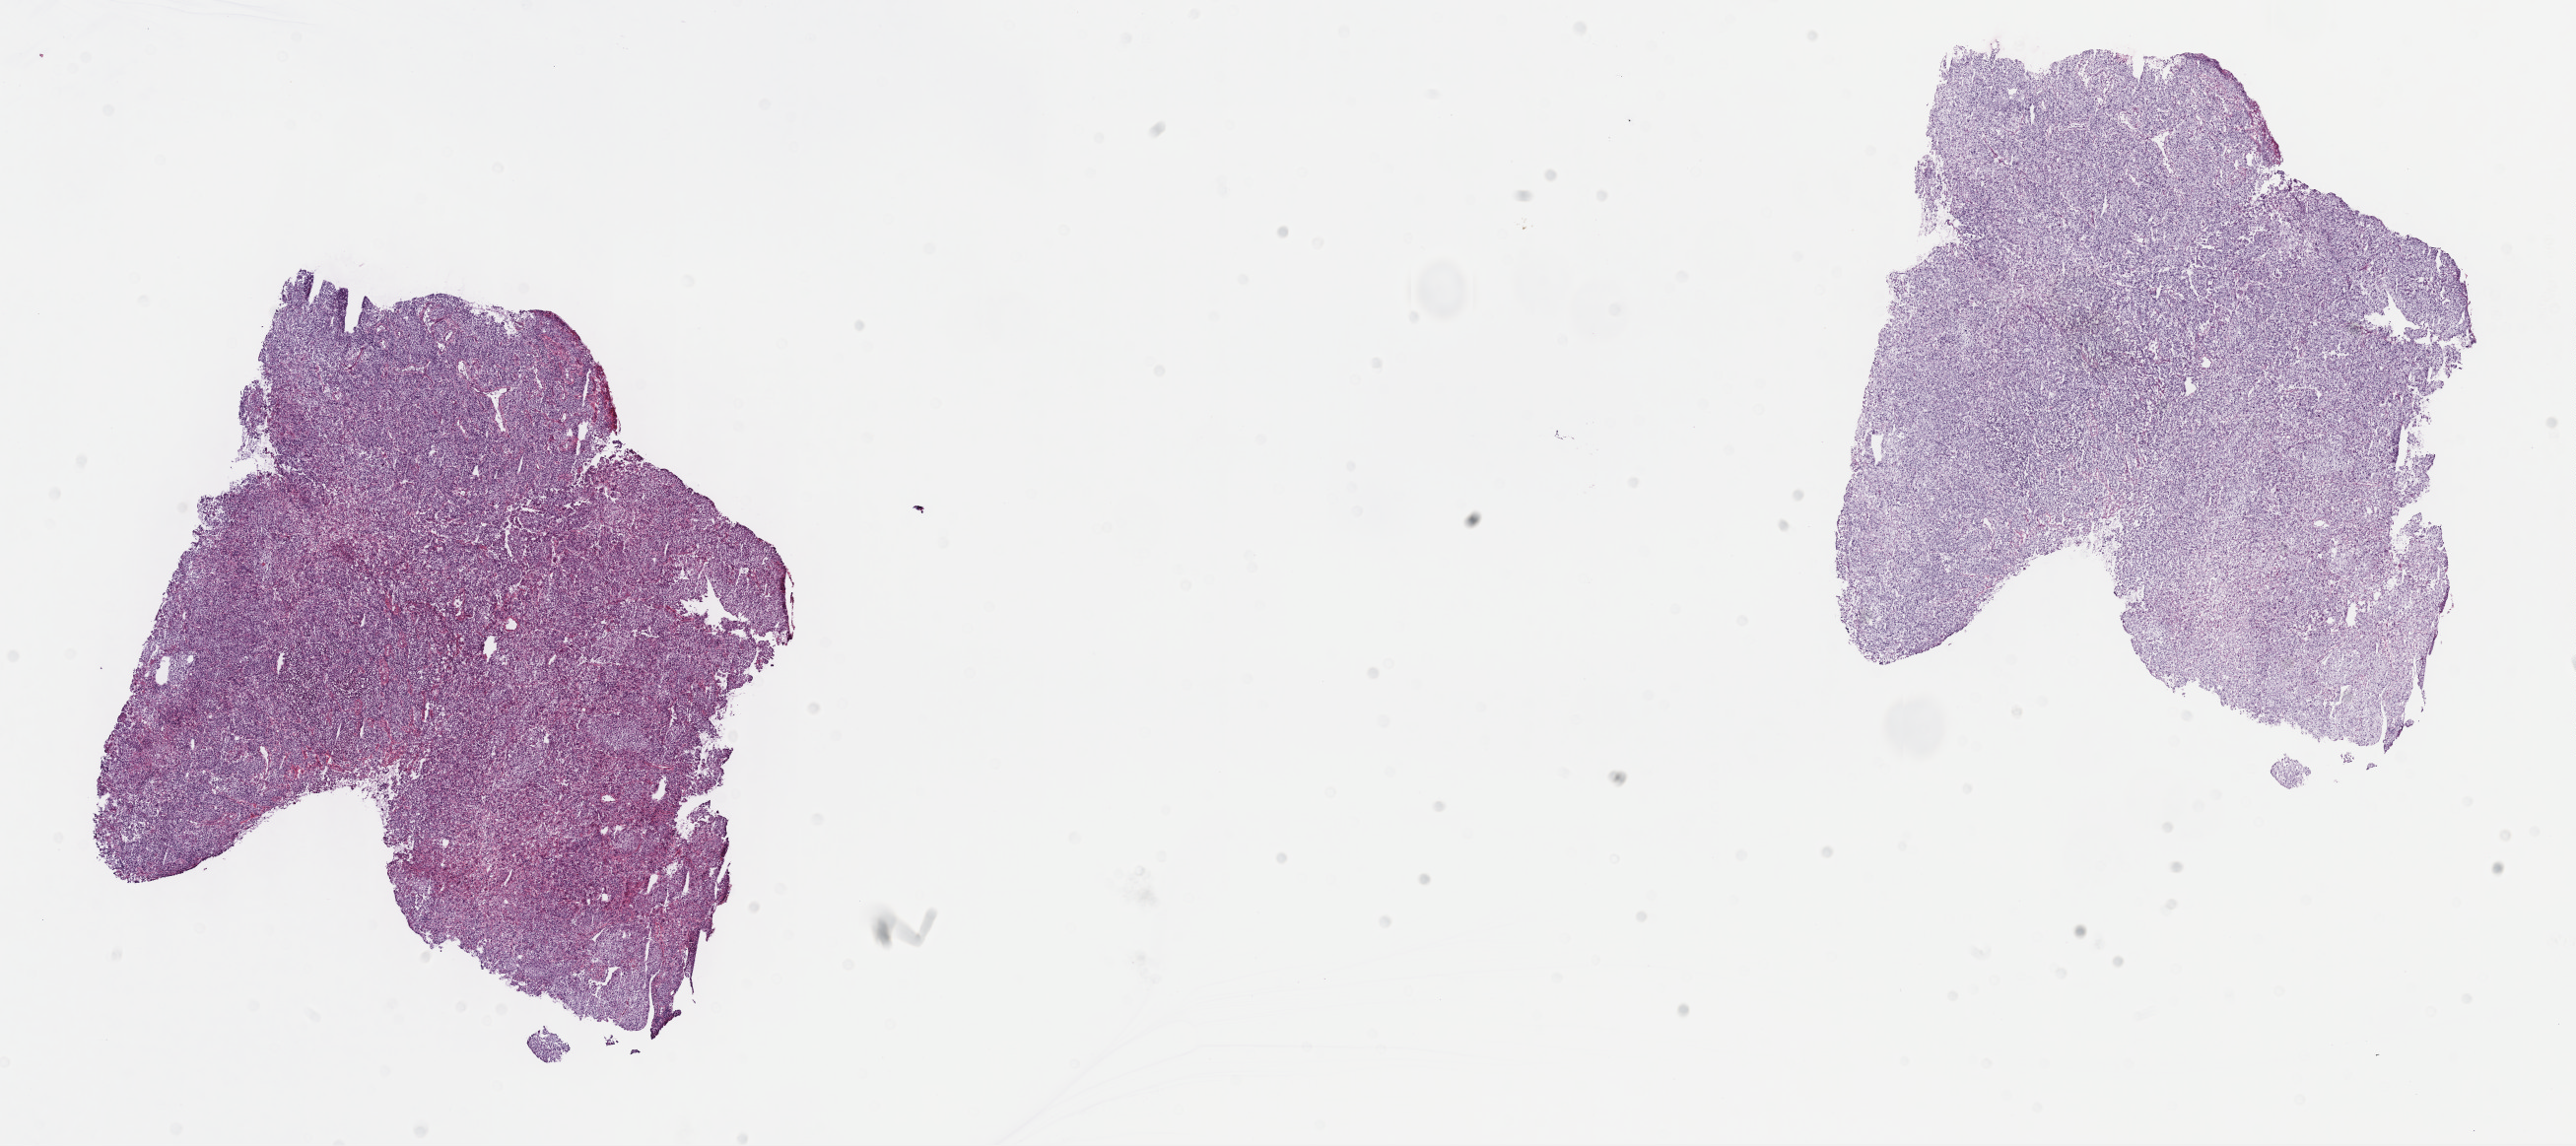
Digitized H&E-stained tissue section (whole slide), low-resolution overview of the scanned area, about 21.1 x 9.4 mm (acquisition: 40x scan); frozen section from the top of the tissue portion; sample: primary tumour, cervix. Female, age 32 years at initial diagnosis. Histologic grade: G2 (moderately differentiated). Composition of this section per pathologist review: tumour cells 90%, tumour nuclei 90%, normal cells 0%, stromal cells 10%, necrosis 0%. Infiltration values recorded for this section: lymphocyte infiltration 0%, monocyte infiltration 0%, neutrophil infiltration 0%.
* histologic diagnosis: Squamous cell carcinoma, NOS (cervix uteri)
* FIGO stage: IIB